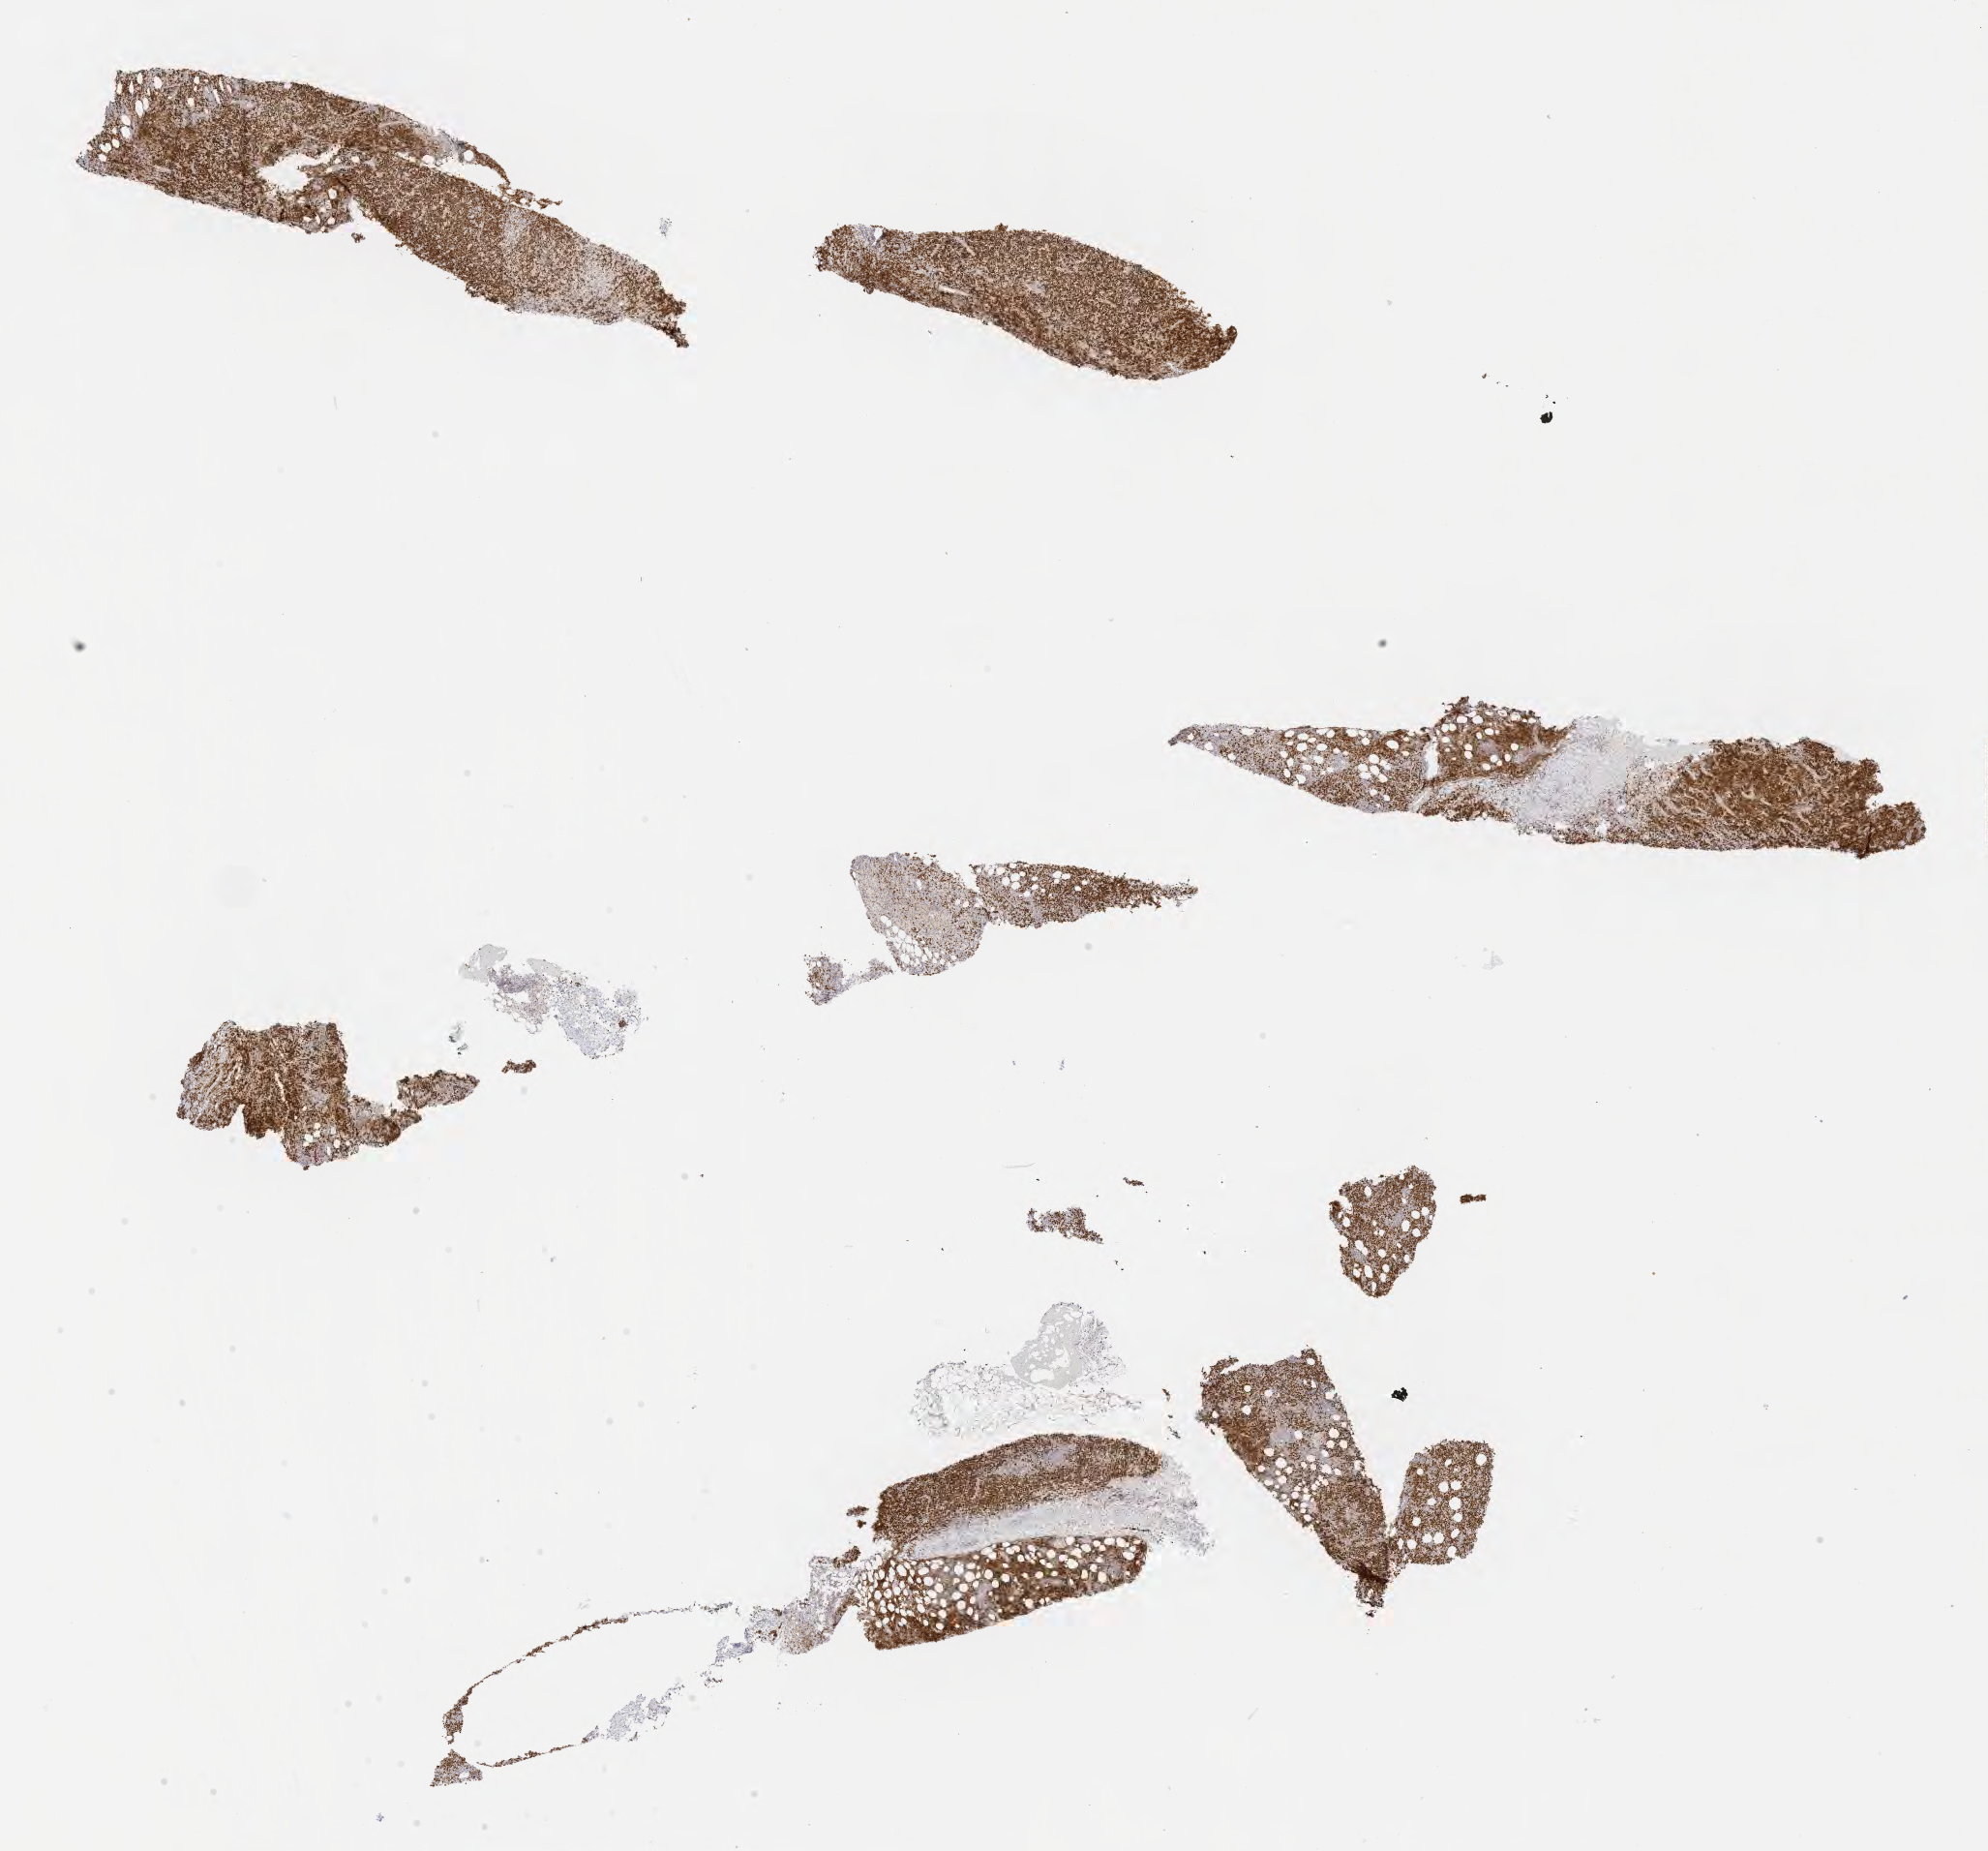
Whole-slide image, immunohistochemical stain for BCL6, a low-resolution overview of the entire scanned area, about 16.6 x 15.5 mm; tumor tissue. Male patient, age 33 years.
• diagnosis: Burkitt lymphoma, NOS